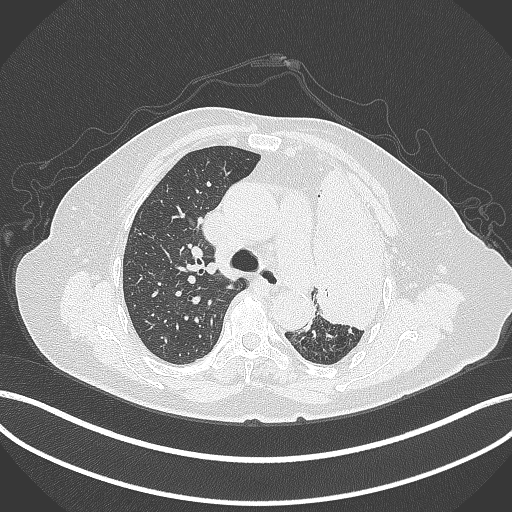
Chest CT, one axial slice; slice 265 of 399 in the series (ordered by position); lung window (W 1500 / L -600 HU); 1 mm slice thickness; 512 × 512 image matrix, field of view 400 × 400 mm. Female patient, age 75 years. Case-level facts recorded for this patient, not image findings: clinical TNM (as recorded): T3 N3 M1.
Structures marked on this image (rectangle marked by the reading radiologist):
- lung tumour (recorded histology: adenocarcinoma): bounding box (x1, y1, x2, y2) in pixels: (305, 151, 398, 332)